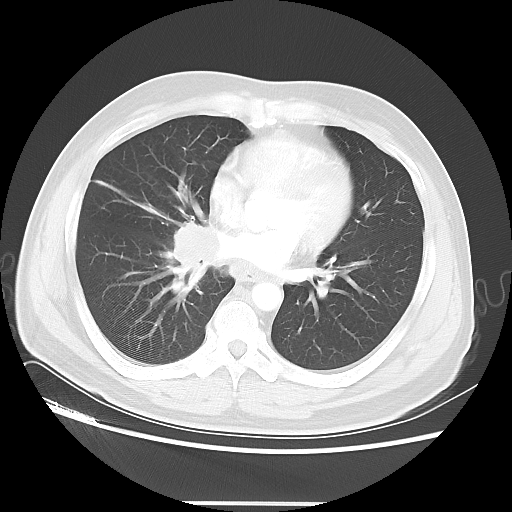
Chest CT, one axial slice; position 20 of 48 along the scan axis; reconstruction kernel LUNG; lung window (W 1500 / L -600 HU); 5 mm slice thickness; 512 × 512 image matrix, field of view 390 × 390 mm. Male patient, age 53 years. Case-level facts recorded for this patient, not image findings: clinical TNM (as recorded): T2 N3 M0; histopathological grade: G3.
Annotated regions visible in this slice (rectangle marked by the reading radiologist):
- lung tumour (recorded histology: small cell carcinoma): bounding box [x1, y1, x2, y2] px = [164, 221, 213, 296]